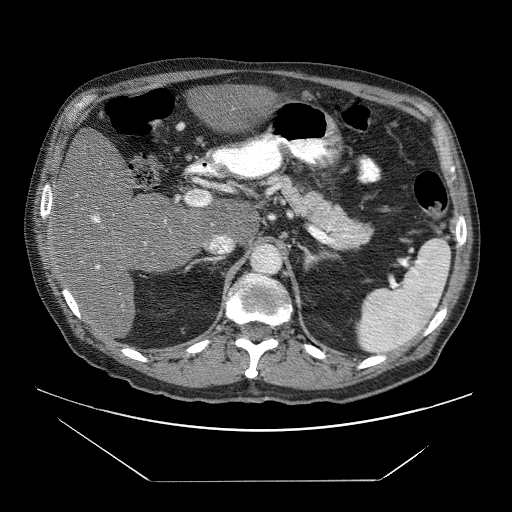
Contrast-enhanced abdominal CT (liver protocol), one axial slice. Soft-tissue window (W 400 / L 40 HU). 512 × 512 image matrix. Case-level facts recorded for this patient, not image findings: diagnosis: hepatocellular carcinoma (patient treated with transarterial chemoembolisation; whether this scan precedes or follows treatment is not stated here); TNM stage (as recorded): Stage-IVB; Child-Pugh class: B; tumour nodularity: uninodular.
Annotated regions visible in this slice (semi-automatic segmentation, software-assisted and operator-edited):
- liver parenchyma outside the tumour (the mass and vessels are separate outlines, so this box may not span the whole liver): bounding box [x1, y1, x2, y2] px = [48, 83, 280, 340]
- liver vessels: [91, 215, 166, 269]